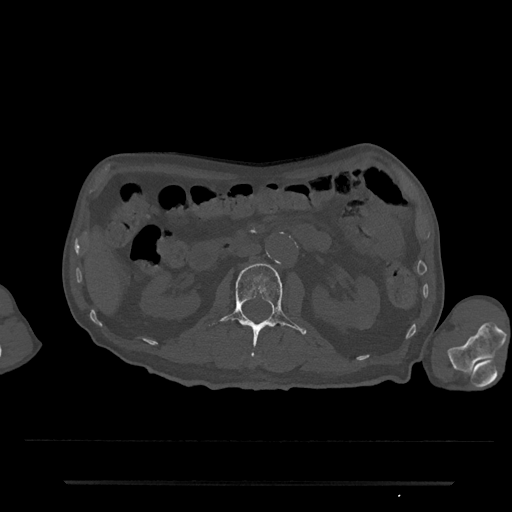
CT including the spine, one axial slice. Position 65 of 797 along the scan axis. Reconstruction kernel Br40s/3. 120 kVp. Bone window (W 1800 / L 400 HU). 0.5 mm slice thickness. 512 × 512 image matrix, field of view 427 × 427 mm. Male patient, age 74 years. From the clinical record (not read from this slice): primary cancer: prostate.
Structures marked on this image (semi-automatic segmentation, software-assisted and operator-edited):
- L2 vertebra: bounding box (x1, y1, x2, y2) in pixels: (209, 263, 307, 344)